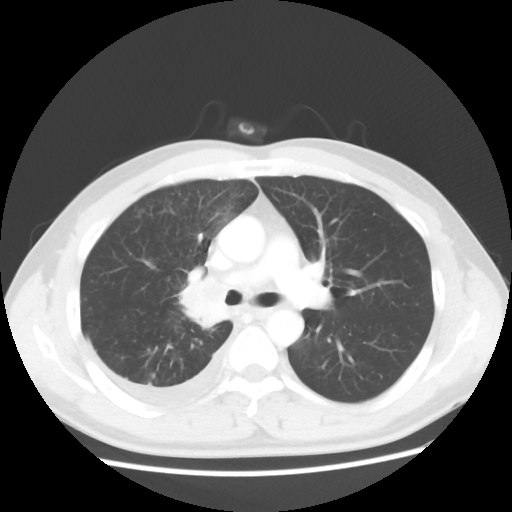
Chest CT, one axial slice. Position 34 of 56 along the scan axis. Reconstruction kernel STANDARD. 120 kVp. Lung window (W 1500 / L -600 HU). 5 mm slice thickness. 512 × 512 image matrix, field of view 360 × 360 mm. Patient: male, 46 years. Case-level facts recorded for this patient, not image findings: clinical TNM (as recorded): T2 N3 M1.
Annotated regions visible in this slice (rectangle marked by the reading radiologist):
- lung tumour (recorded histology: adenocarcinoma): bounding box <175,269,230,339> (left, top, right, bottom; pixels)